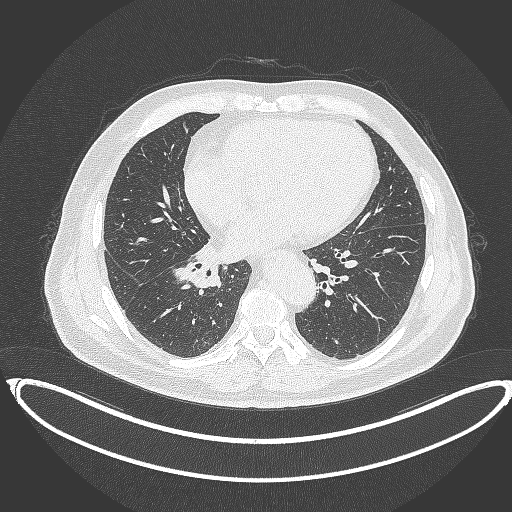
Chest CT, one axial slice. Reconstruction kernel B70f. 120 kVp. Lung window (W 1500 / L -600 HU). 1 mm slice thickness. 512 × 512 image matrix, field of view 448 × 448 mm. Patient: male, 61 years. Case-level facts recorded for this patient, not image findings: clinical TNM (as recorded): T1b N1 M0.
Outlined on this slice (rectangle marked by the reading radiologist):
- lung tumour (recorded histology: squamous cell carcinoma): bounding box [x1, y1, x2, y2] px = [171, 260, 221, 291]